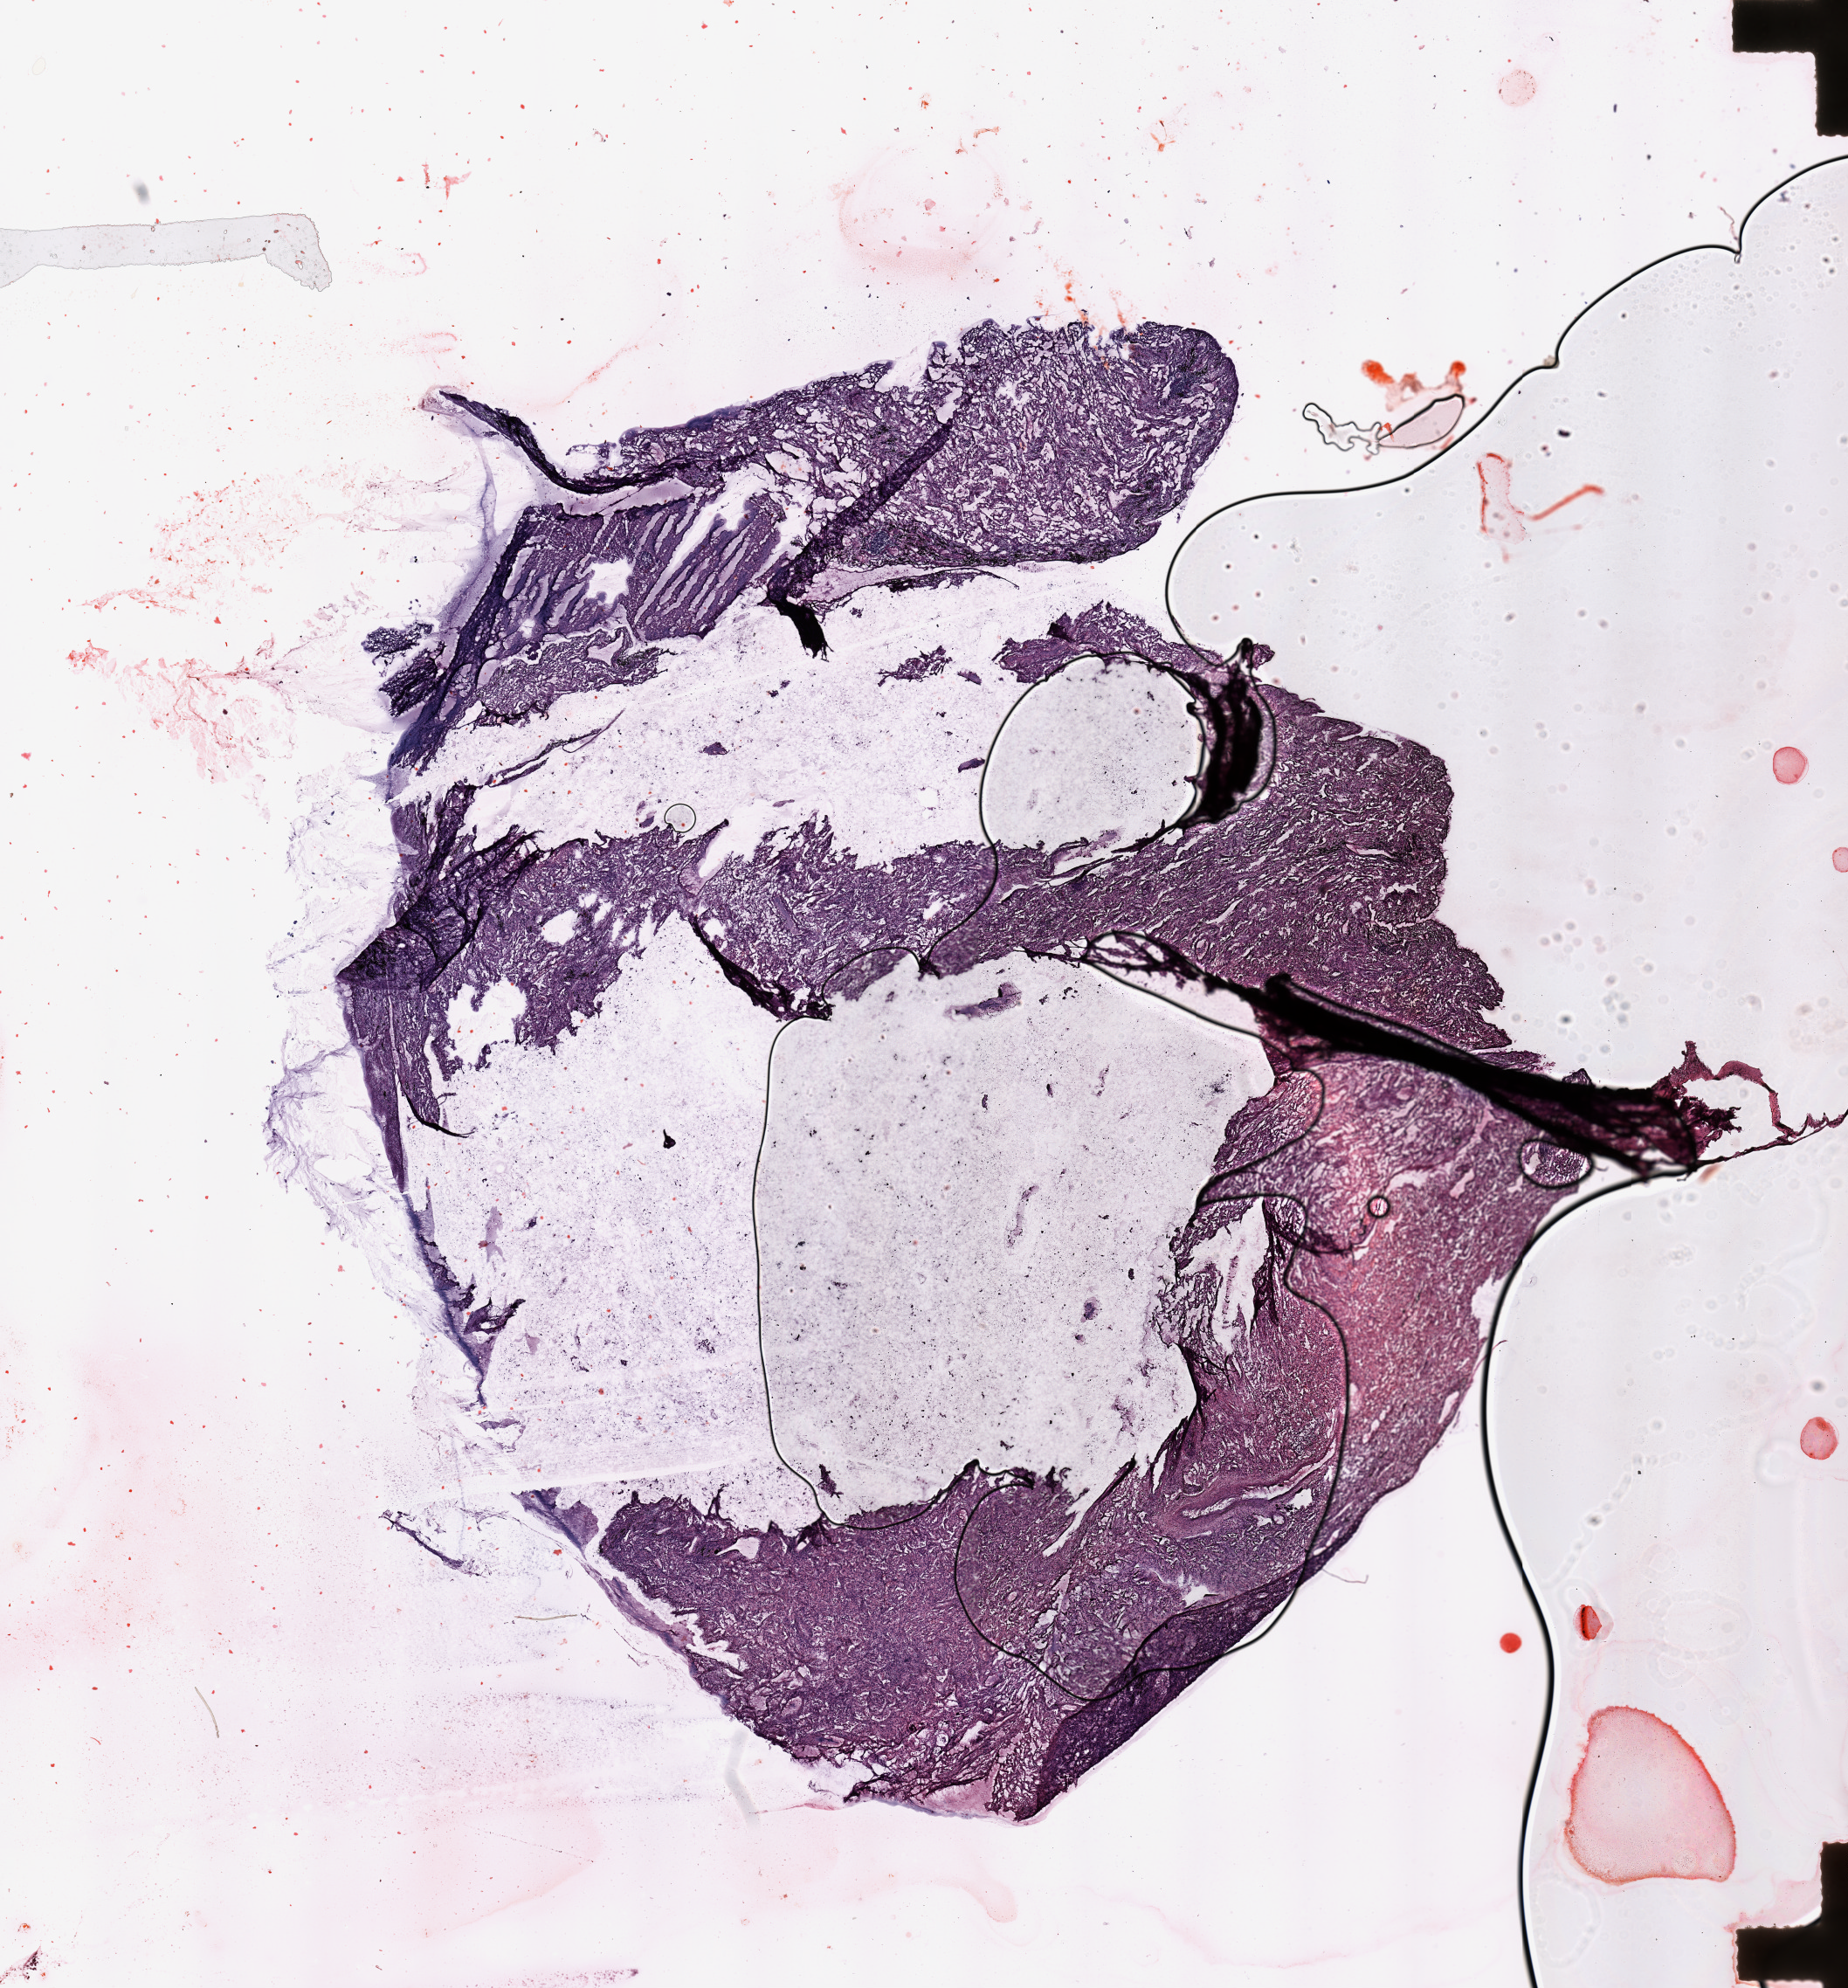
Digitized H&E tissue section (whole slide), low-resolution overview of the scanned area, about 16.7 x 18.0 mm (slide scanned at 20x). Lung, normal (non-tumour) tissue. Patient: male, age 67 years.
This section: normal (non-tumour) tissue from the same patient. Patient diagnosis (cohort enrolment): squamous cell carcinoma (lung).